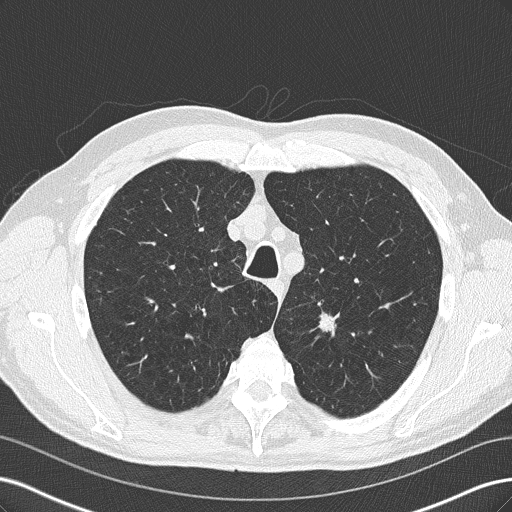
Chest CT (low-dose screening protocol), one axial image, third screening round (two years after baseline), lung window (W 1500 / L -600 HU), 120 kVp, slice 43 of 219 in the series. Male, age 66 years at enrolment. Current smoker at enrolment.
• Expert reader's lesion annotation, bounding box <297,302,351,347> (left, top, right, bottom; pixels).
• The exam's reader record, not a measurement of the box and not confirmed to be the same lesion: non-calcified nodule or mass ≥4 mm, left upper lobe, 14 × 9 mm, spiculated (stellate) margins, soft tissue attenuation, pre-existing on the prior screen: yes; interval growth: yes.